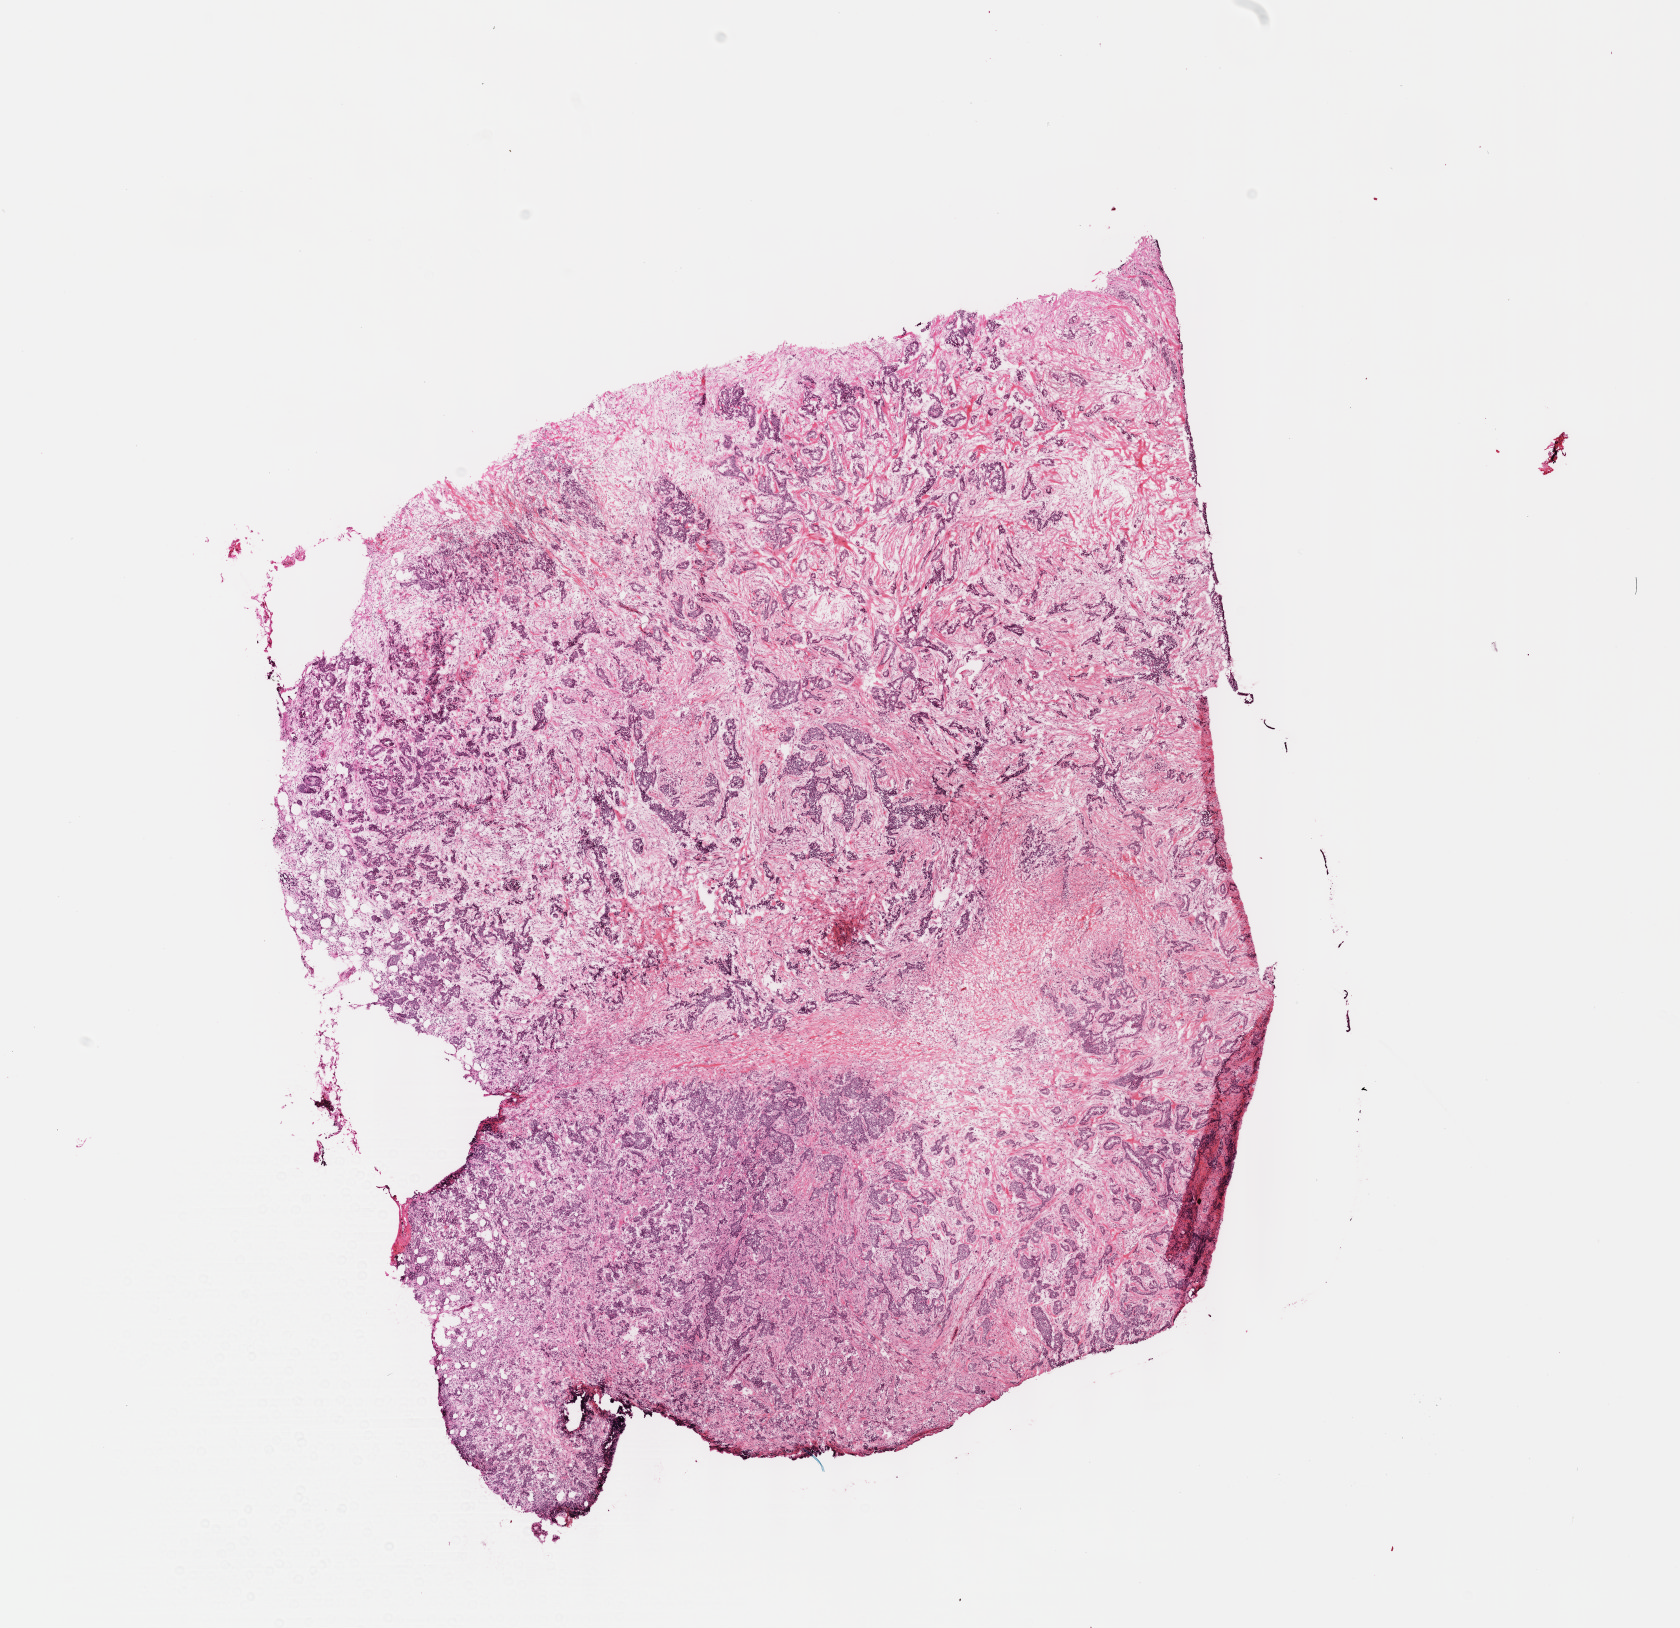
Whole-slide histology image, H&E, whole scanned area (about 13.6 x 13.2 mm, slide scanned at 40x) shown as a low-resolution overview; formalin-fixed paraffin-embedded (FFPE) diagnostic section; primary tumour sample from the breast. Female patient; age at initial diagnosis 71 years.
Histologic diagnosis: Infiltrating duct carcinoma, NOS. AJCC pathologic stage: IIA. TNM: T2 N0 M0.